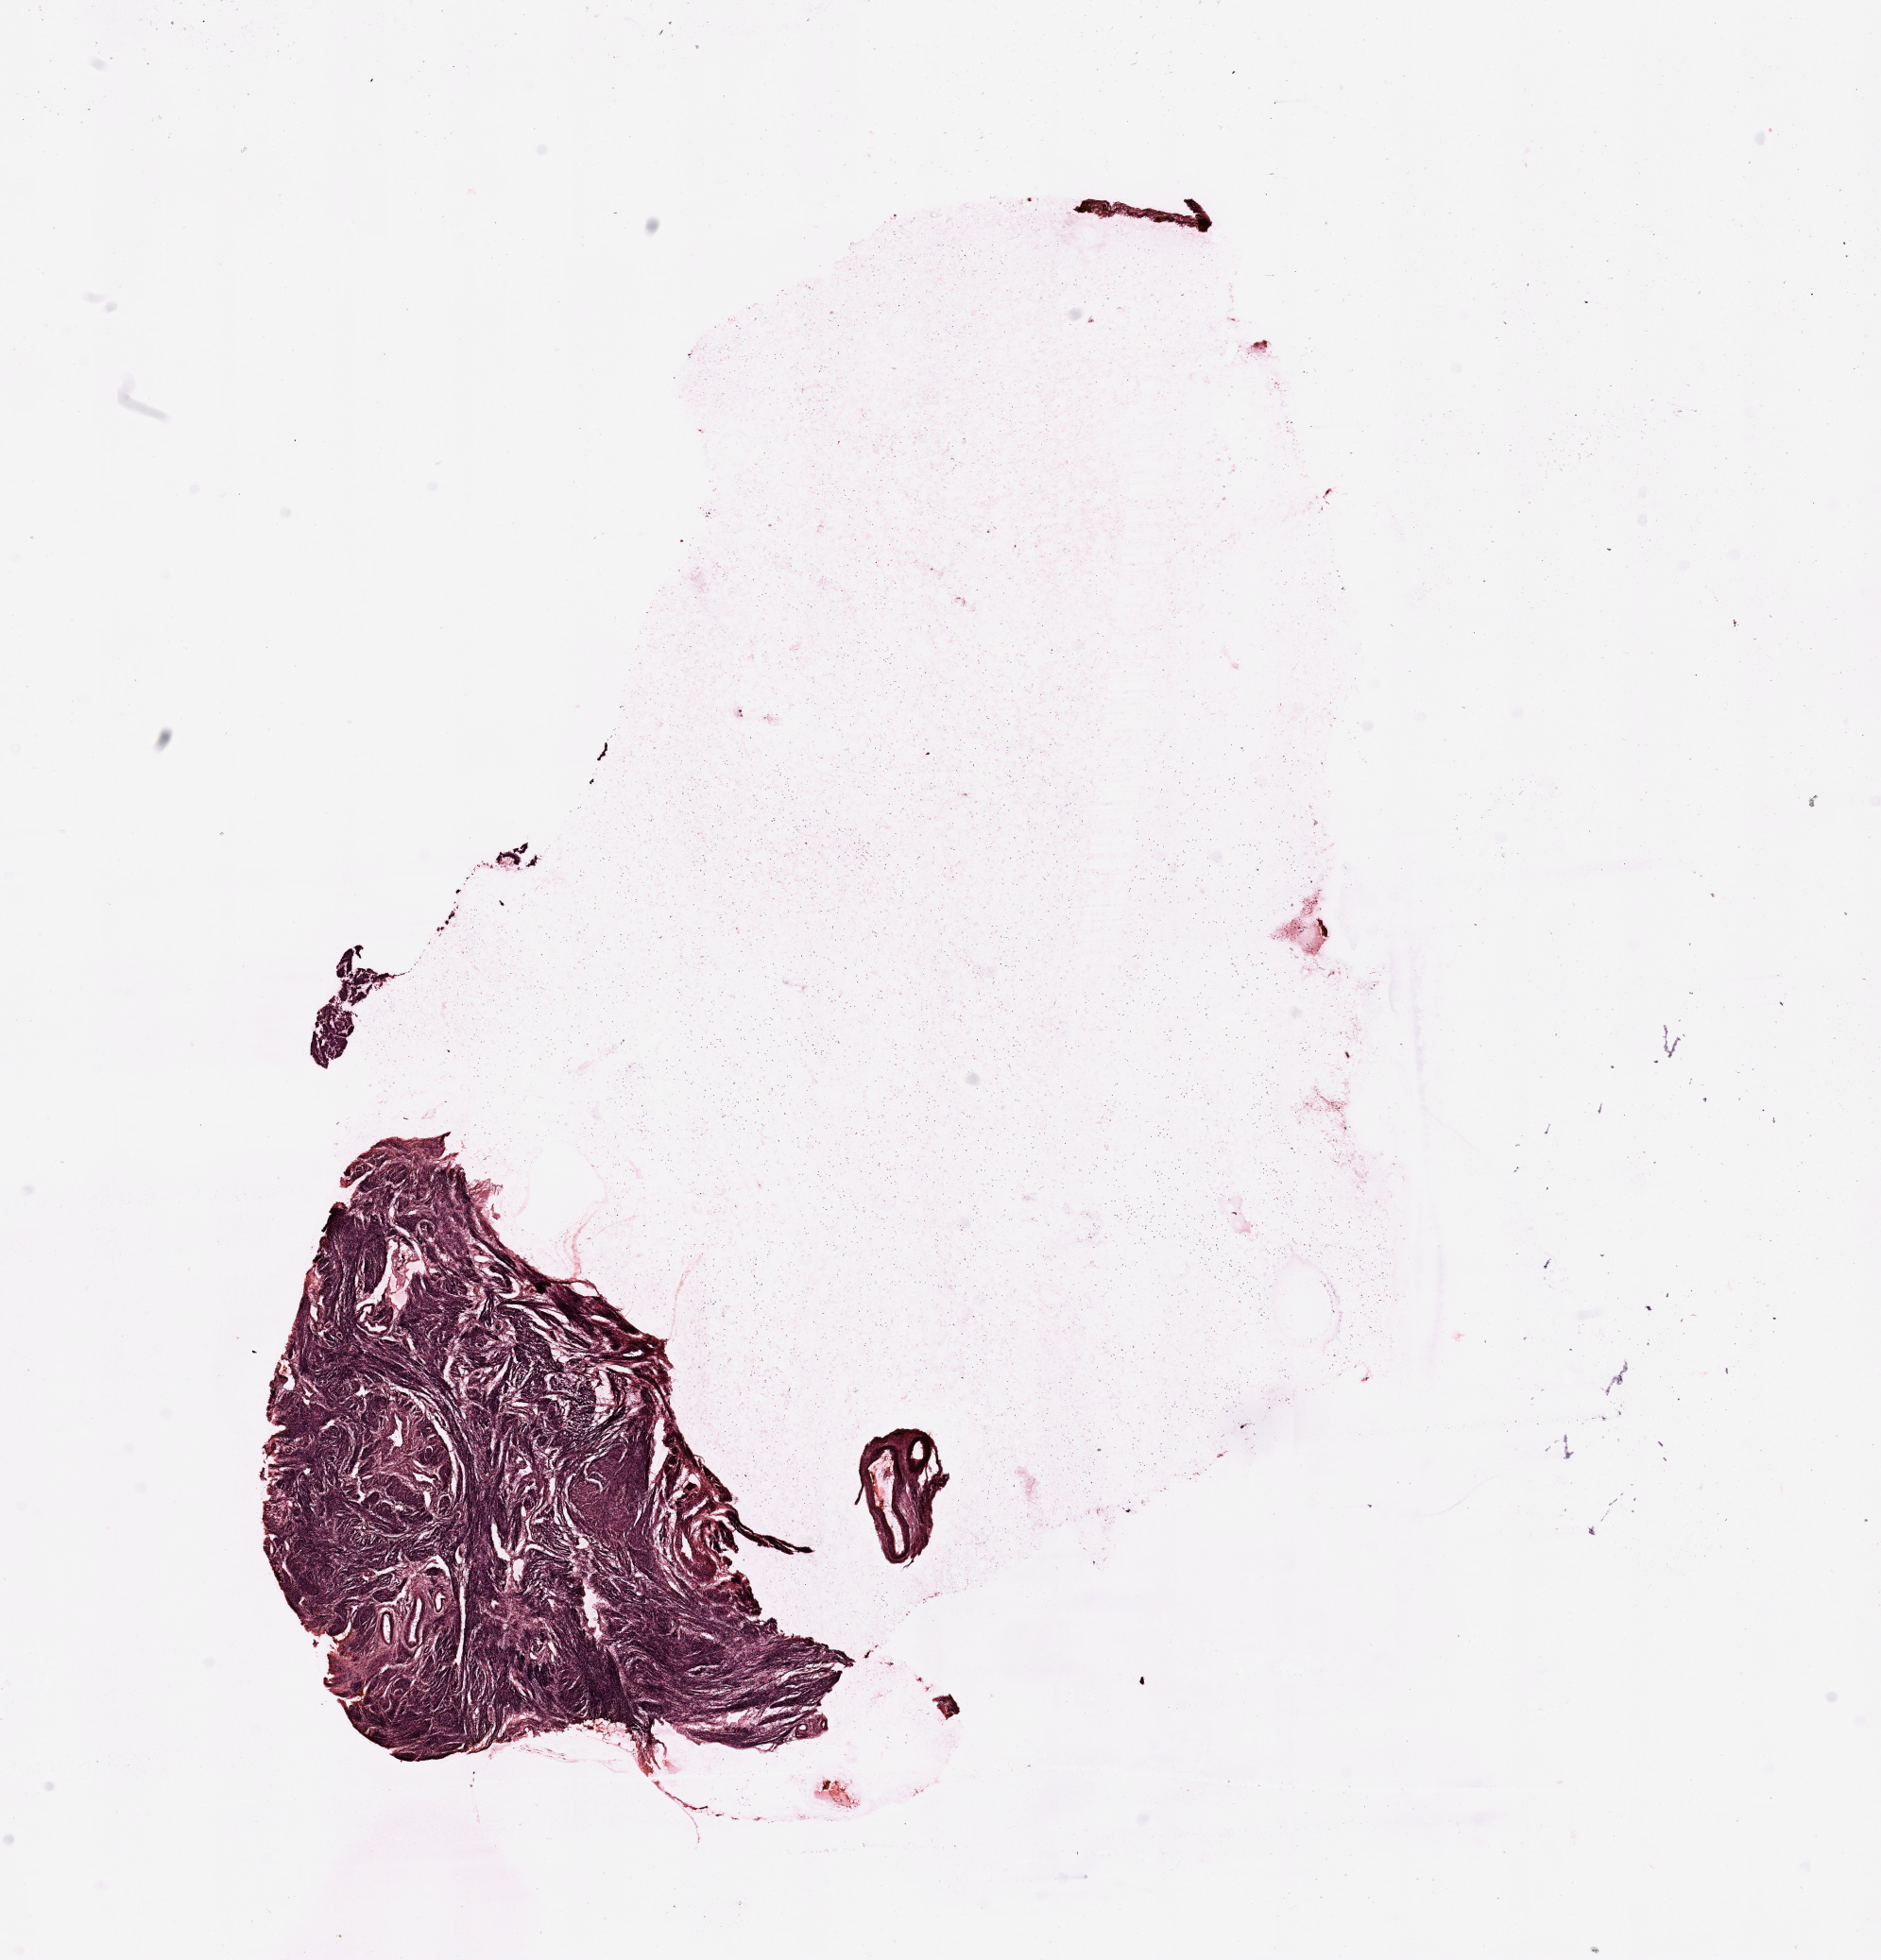
Whole-slide histology image, Hematoxylin and eosin (H&E) stained, shown as a low-resolution overview of the whole scanned area (about 15.8 x 16.4 mm), normal (non-tumour) tissue sample, uterus. Female, 66 y/o.
This section: normal (non-tumour) tissue from the same patient. Patient diagnosis: Endometrioid adenocarcinoma, NOS.